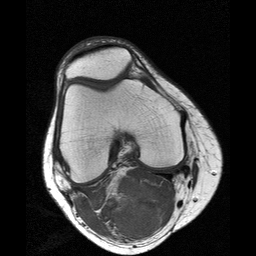
MRI of an extremity soft-tissue mass, one axial slice; 256 × 256 image matrix. Female patient. From the clinical record (not read from this slice): histological type: liposarcoma; site of the primary tumour: right thigh.
Annotated regions visible in this slice (expert manual segmentation):
- gross tumour volume (mass): bounding box [x1, y1, x2, y2] px = [96, 174, 161, 238]